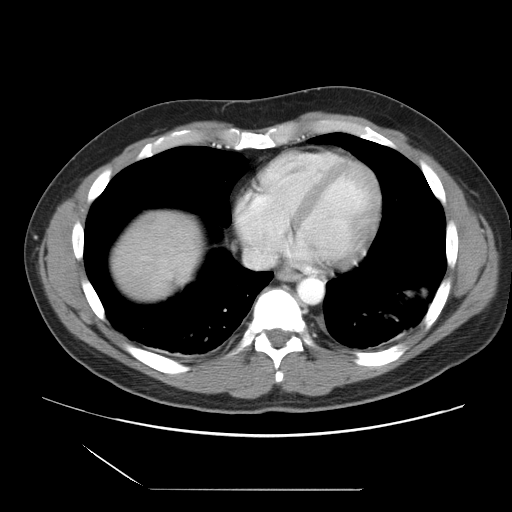
Contrast-enhanced abdominal CT, one axial slice. Position 33 of 39 along the scan axis. 120 kVp. Intravenous contrast given. Soft-tissue window (W 400 / L 40 HU). 5 mm slice thickness. 512 × 512 image matrix, field of view 395 × 395 mm. Male patient, age 39 years. Case-level facts recorded for this patient, not image findings: diagnosis: colorectal cancer liver metastases, imaged before liver resection; multiple liver metastases: yes; largest metastasis: 1.3 cm; disease in both lobes: no.
Structures marked on this image (manually delineated by an expert):
- liver: bounding box [x1, y1, x2, y2] px = [112, 211, 205, 302]